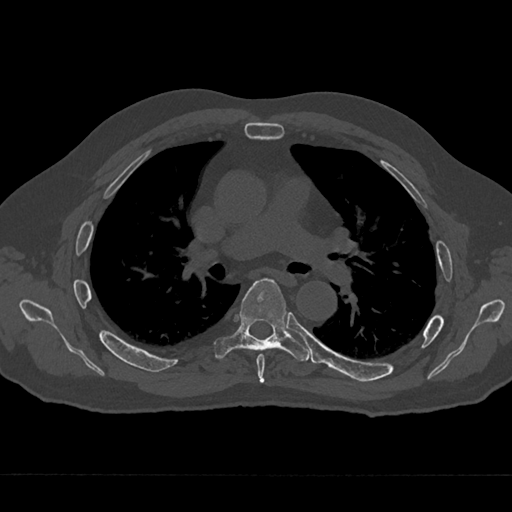
CT including the spine, one axial slice. Slice 436 of 797 in the series (ordered by position). Reconstruction kernel Br40s/3. 120 kVp. Bone window (W 1800 / L 400 HU). 512 × 512 image matrix. Male patient, age 75 years. From the clinical record (not read from this slice): primary cancer: renal; vertebrae with lytic lesions (as recorded): T4.
Annotated regions visible in this slice (semi-automatically segmented with operator editing):
- T5 vertebra: bounding box <256,354,265,383> (left, top, right, bottom; pixels)
- T6 vertebra: <213,278,310,361>